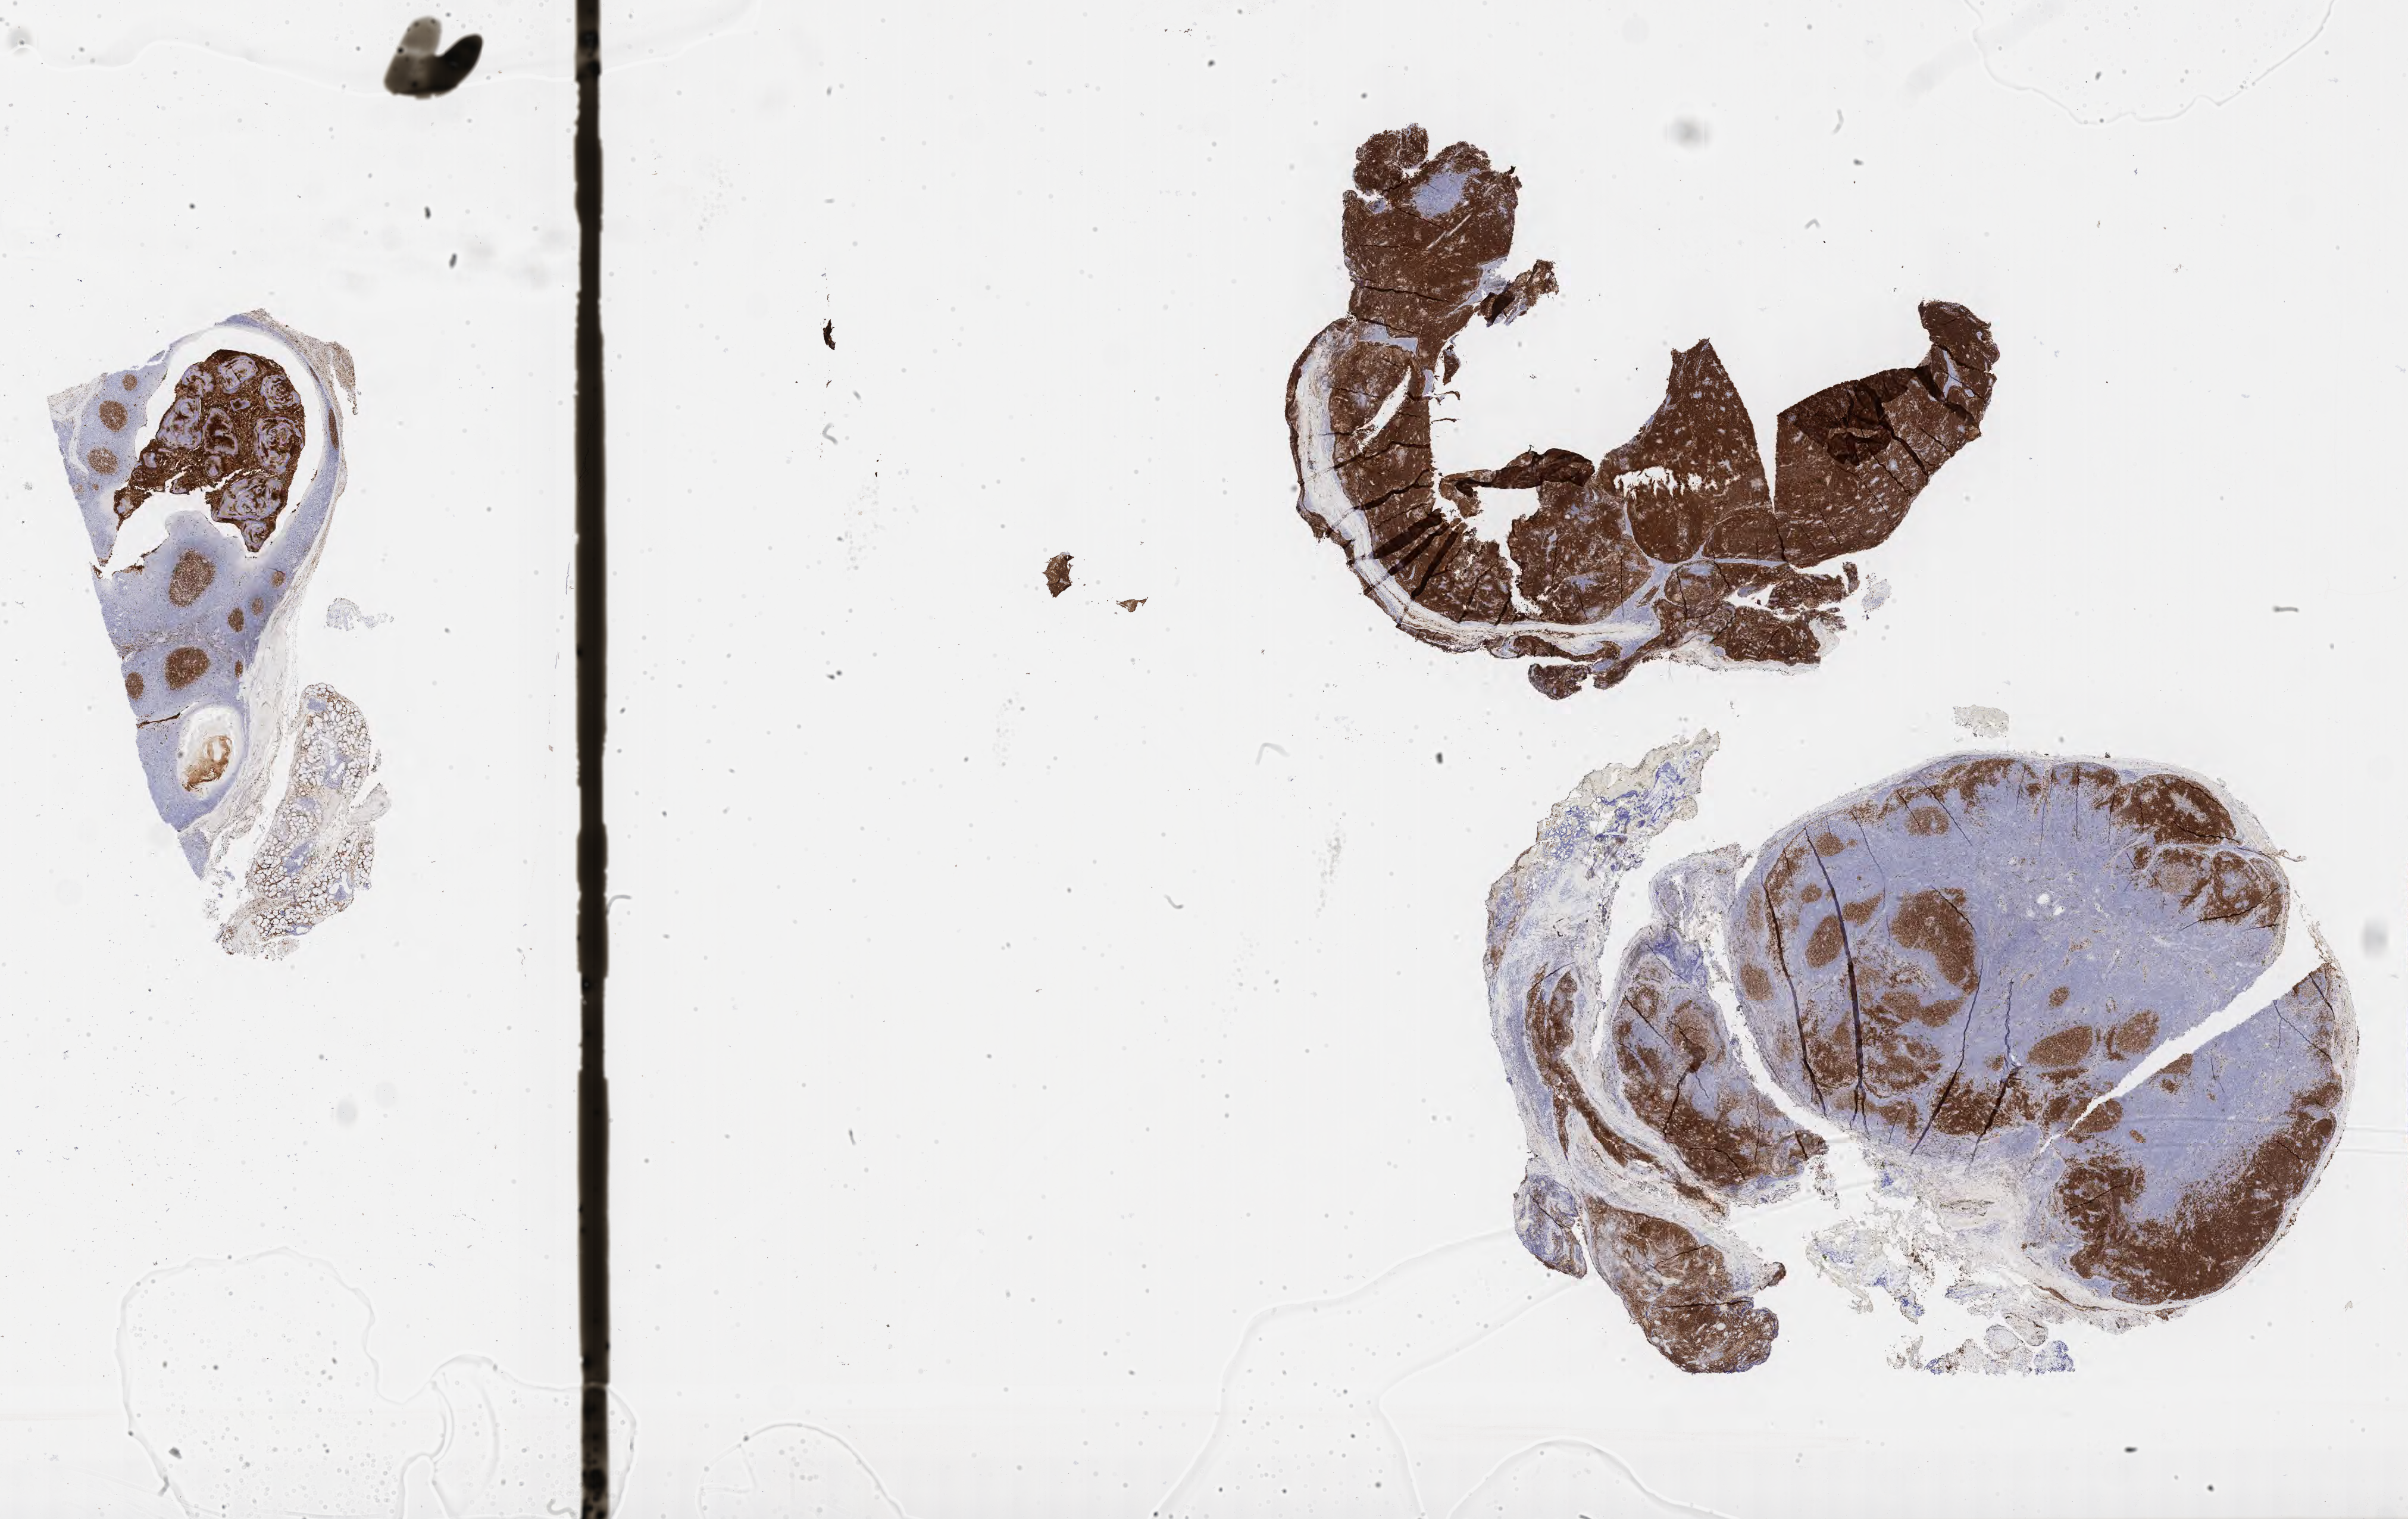
Whole-slide image, immunohistochemical stain for CD10 — low-resolution overview of the scanned area, about 32.7 x 20.6 mm, tumor tissue. Patient male; age 25 years.
Histologic diagnosis: Burkitt lymphoma, NOS.